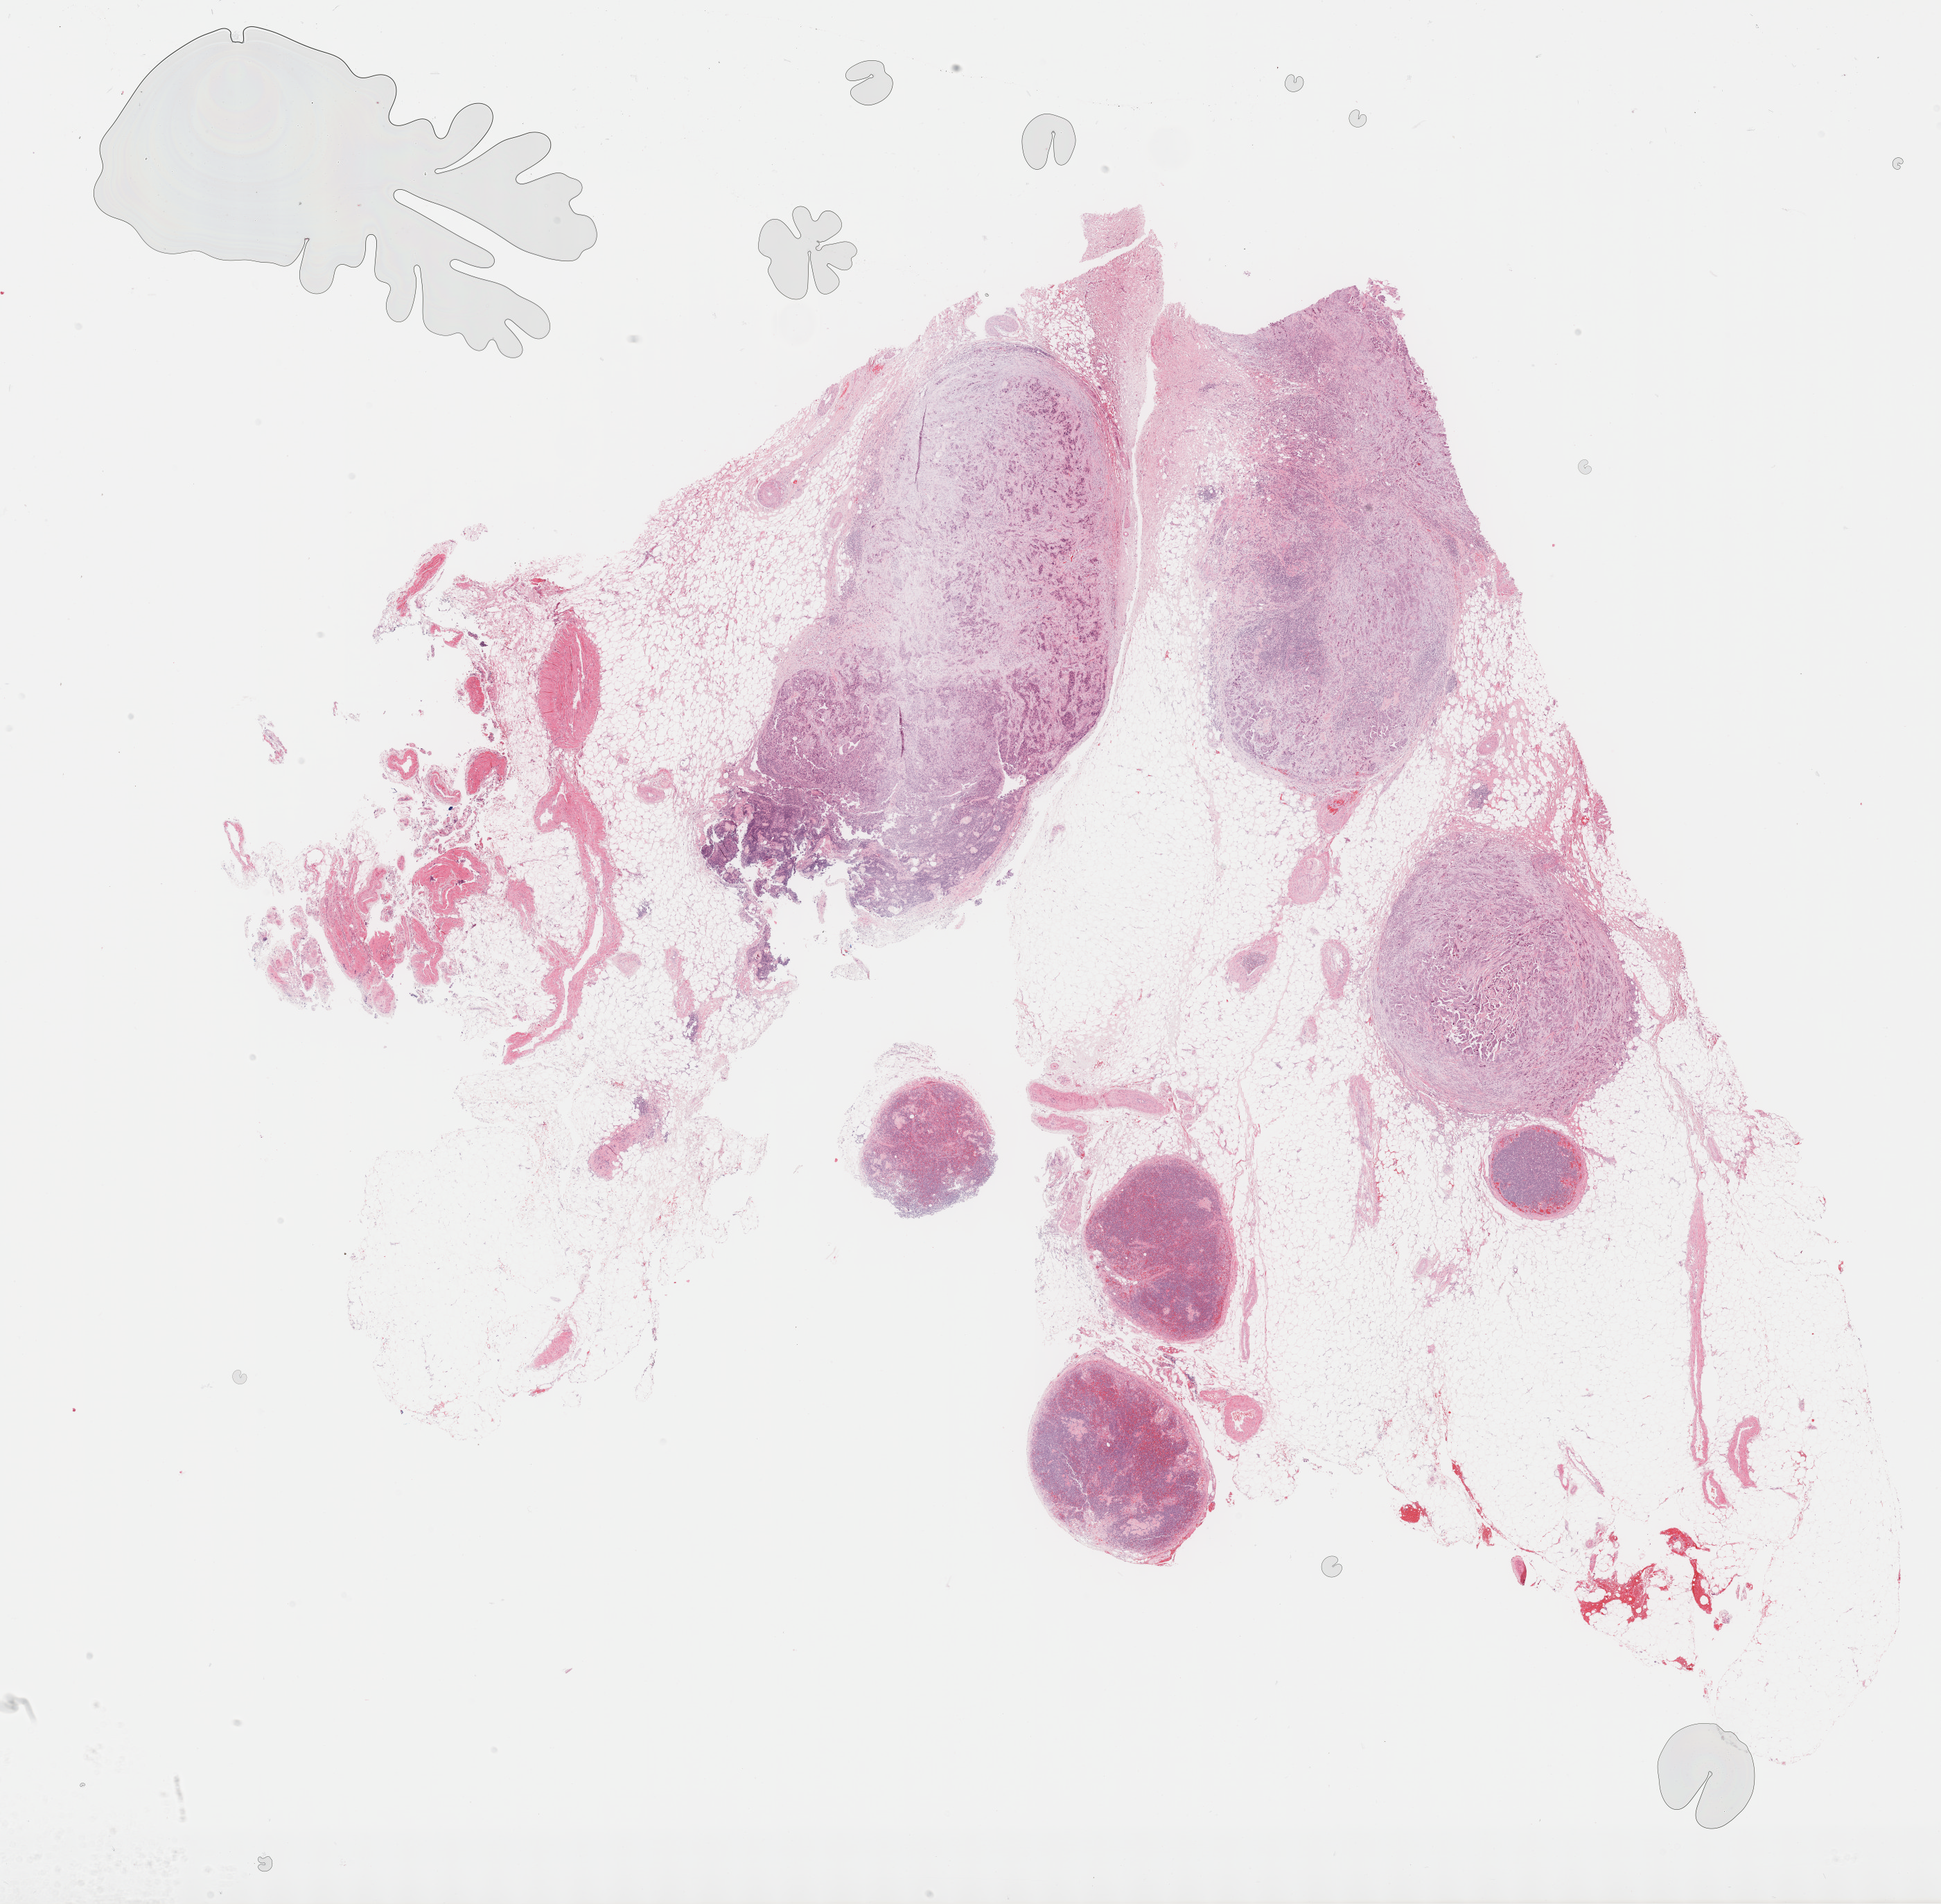
Hematoxylin and eosin (H&E) stained whole-slide image — low-resolution overview of the scanned area, about 22.7 x 22.2 mm; FFPE section; primary tumour sample from the bladder. Patient: male, age at initial diagnosis 65 years. Histologic grade: high grade.
TNM: T4 N2 MX. AJCC pathologic stage: IV (6th edition). Diagnosis: Transitional cell carcinoma.